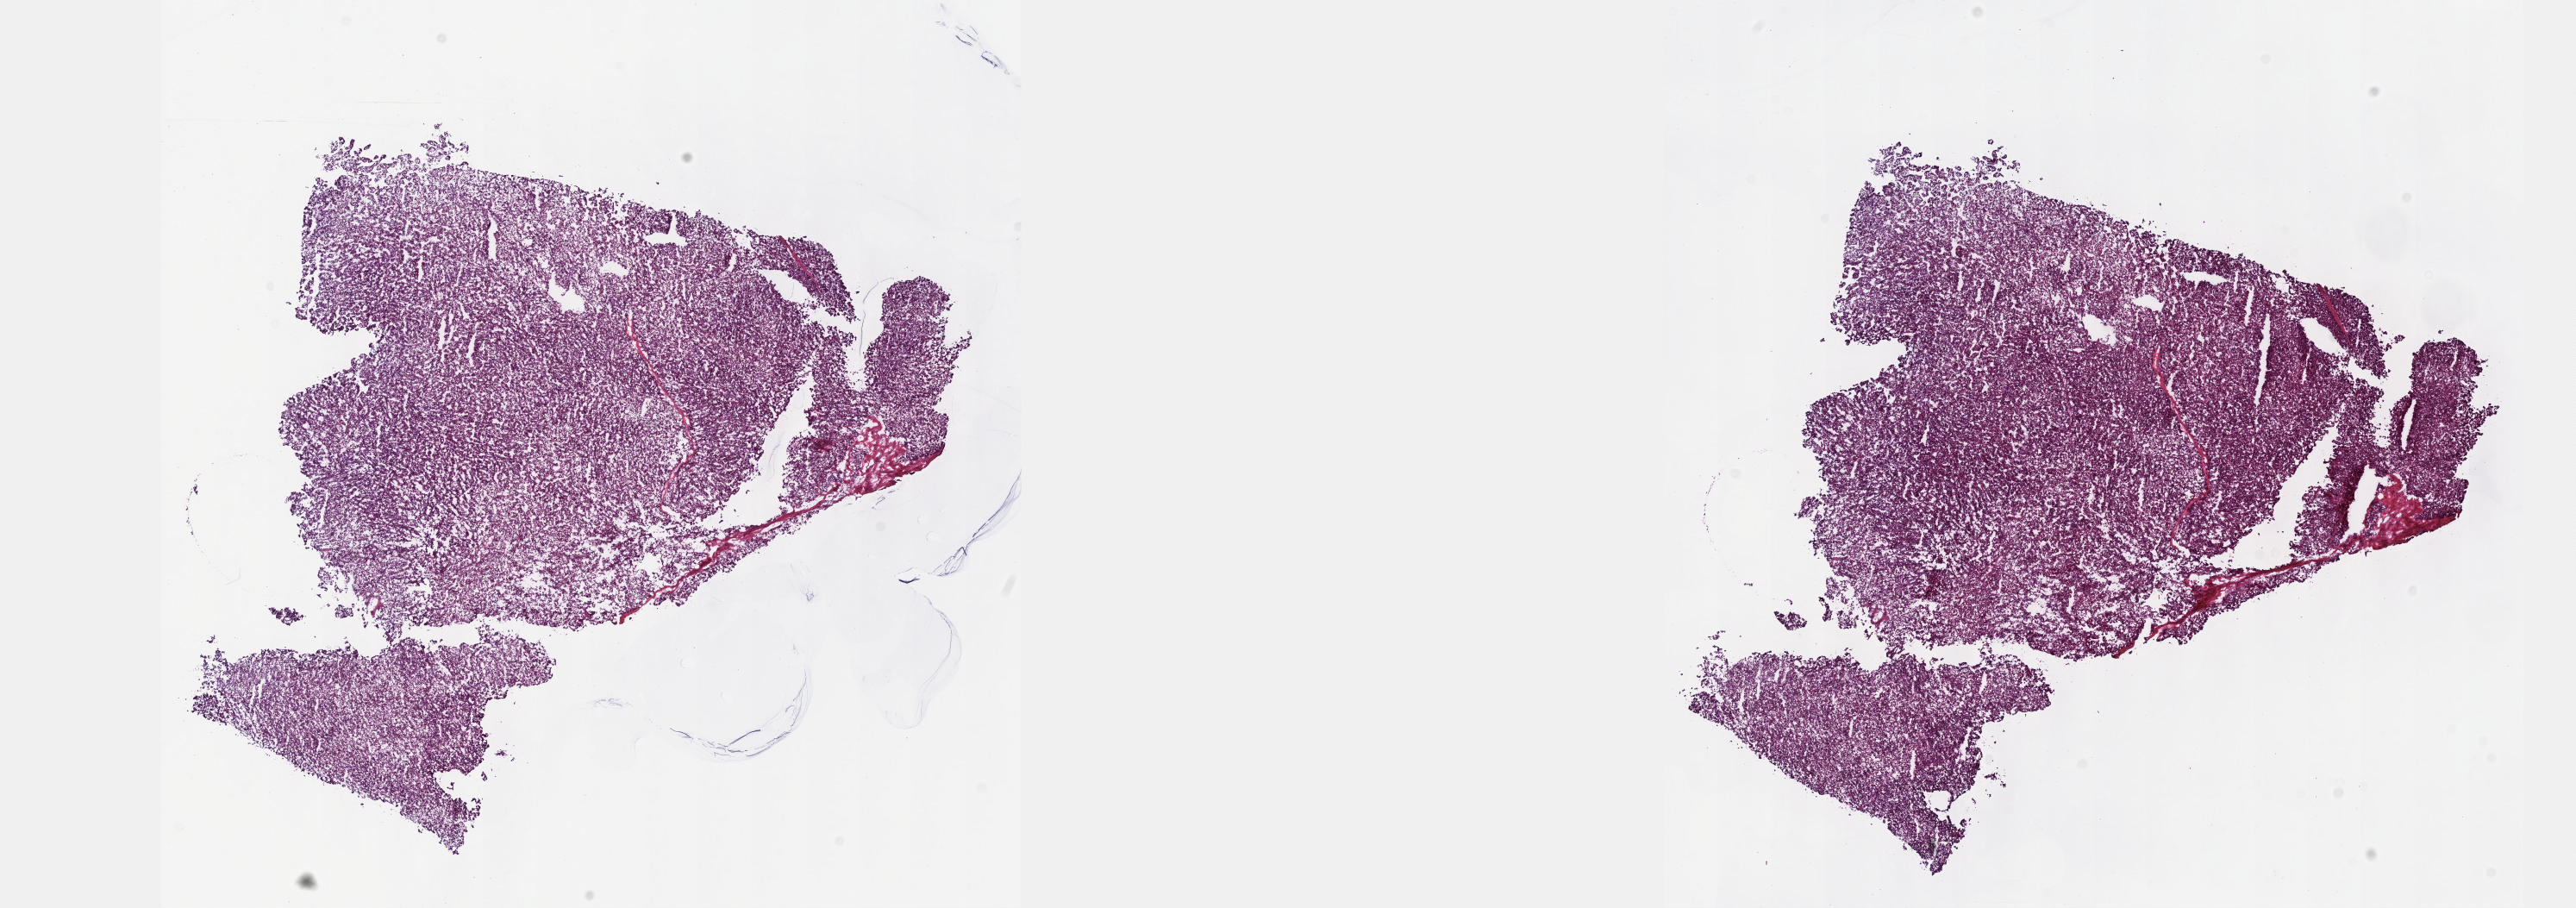
Digitized Hematoxylin and eosin (H&E) stained tissue section (whole slide) — shown as a low-resolution overview of the whole scanned area (about 24.1 x 8.5 mm, acquisition: 40x scan), frozen section from the top of the tissue portion, sample: primary tumour, liver. Male, age 48 years at initial diagnosis. Histologic grade: G2 (moderately differentiated). Composition of this section per pathologist review: tumour cells 95%, tumour nuclei 97%, normal cells 0%, stromal cells 4%, necrosis 1%. Inflammatory infiltration, as recorded: lymphocyte infiltration 2%, monocyte infiltration 0%, neutrophil infiltration 0%.
Diagnosis: Hepatocellular carcinoma, NOS. AJCC pathologic stage: I (7th edition).